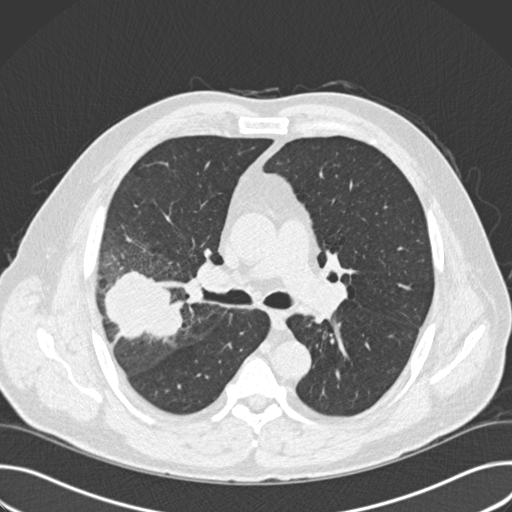
Low-dose screening chest CT, one axial slice; position 100 of 157 along the scan axis; reconstruction kernel B30f; 120 kVp; lung window (W 1500 / L -600 HU); 2 mm slice thickness; 512 × 512 image matrix.
Structures marked on this image (expert manual segmentation):
- lesion 1 (tumor, upper lobe of right lung): bounding box [x1, y1, x2, y2] px = [104, 271, 184, 340]